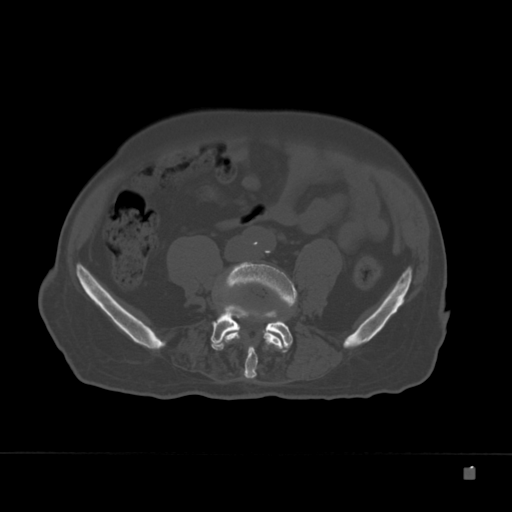
CT including the spine, one axial slice; position 33 of 332 along the scan axis; 120 kVp; bone window (W 1800 / L 400 HU); 1.5 mm slice thickness; 512 × 512 image matrix, field of view 389 × 389 mm. Male patient, age 72 years. From the clinical record (not read from this slice): primary cancer: skeletal.
Outlined on this slice (semi-automatically segmented with operator editing):
- L4 vertebra: bounding box [x1, y1, x2, y2] px = [223, 262, 297, 379]
- L5 vertebra: [211, 304, 293, 351]